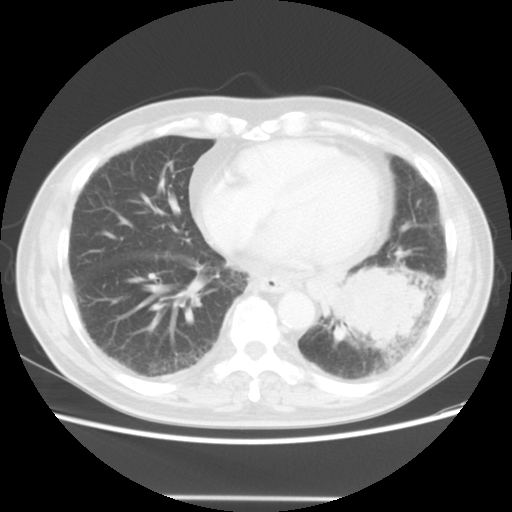
Chest CT, one axial slice. Position 17 of 56 along the scan axis. 140 kVp. Lung window (W 1500 / L -600 HU). 5 mm slice thickness. 512 × 512 image matrix, field of view 360 × 360 mm. Patient: male, 66 years. From the clinical record (not read from this slice): clinical TNM (as recorded): T4 N3 M0.
Annotated regions visible in this slice (rectangle marked by the reading radiologist):
- lung tumour (recorded histology: small cell carcinoma): bounding box (x1, y1, x2, y2) in pixels: (339, 265, 431, 355)